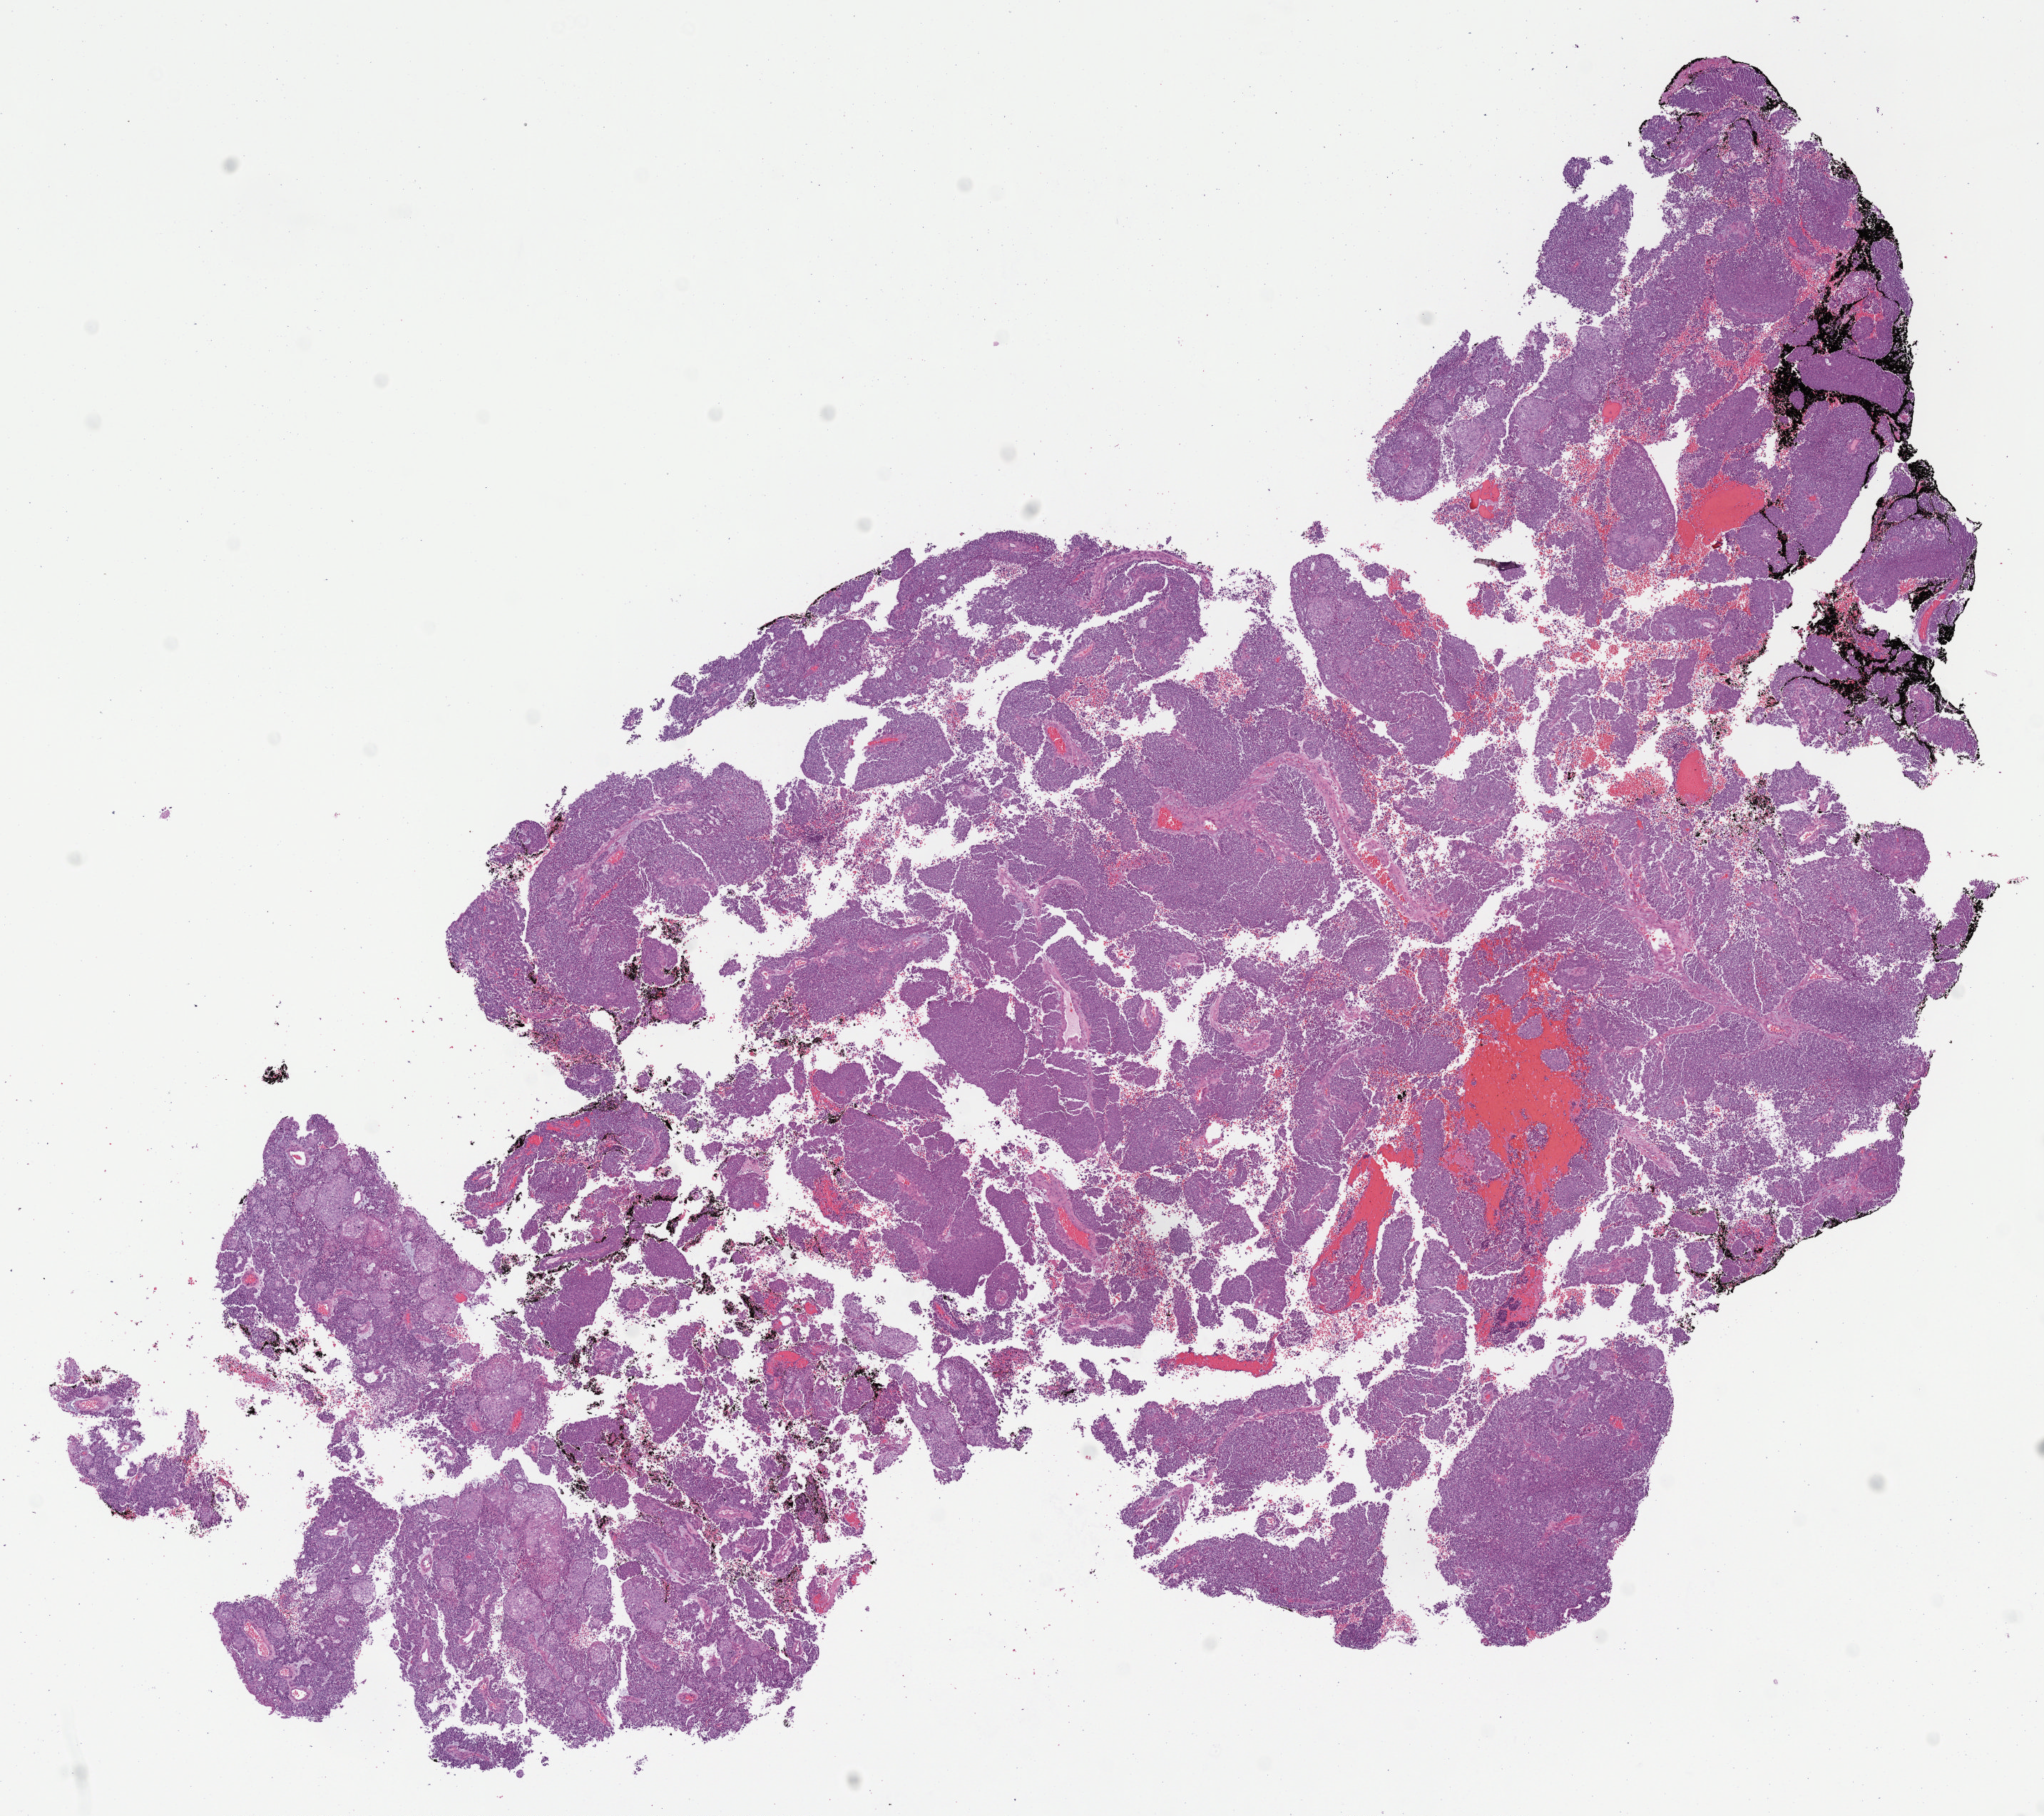
Whole-slide histology image, H&E, shown as a low-resolution overview of the whole scanned area (about 11.6 x 10.3 mm); formalin-fixed paraffin-embedded (FFPE) diagnostic section; sample: primary tumour, uterus. Female patient; age at initial diagnosis 55 years. Histologic grade: G3 (poorly differentiated).
FIGO stage: IIIA. Pathologic diagnosis: Endometrioid adenocarcinoma, NOS (endometrium).